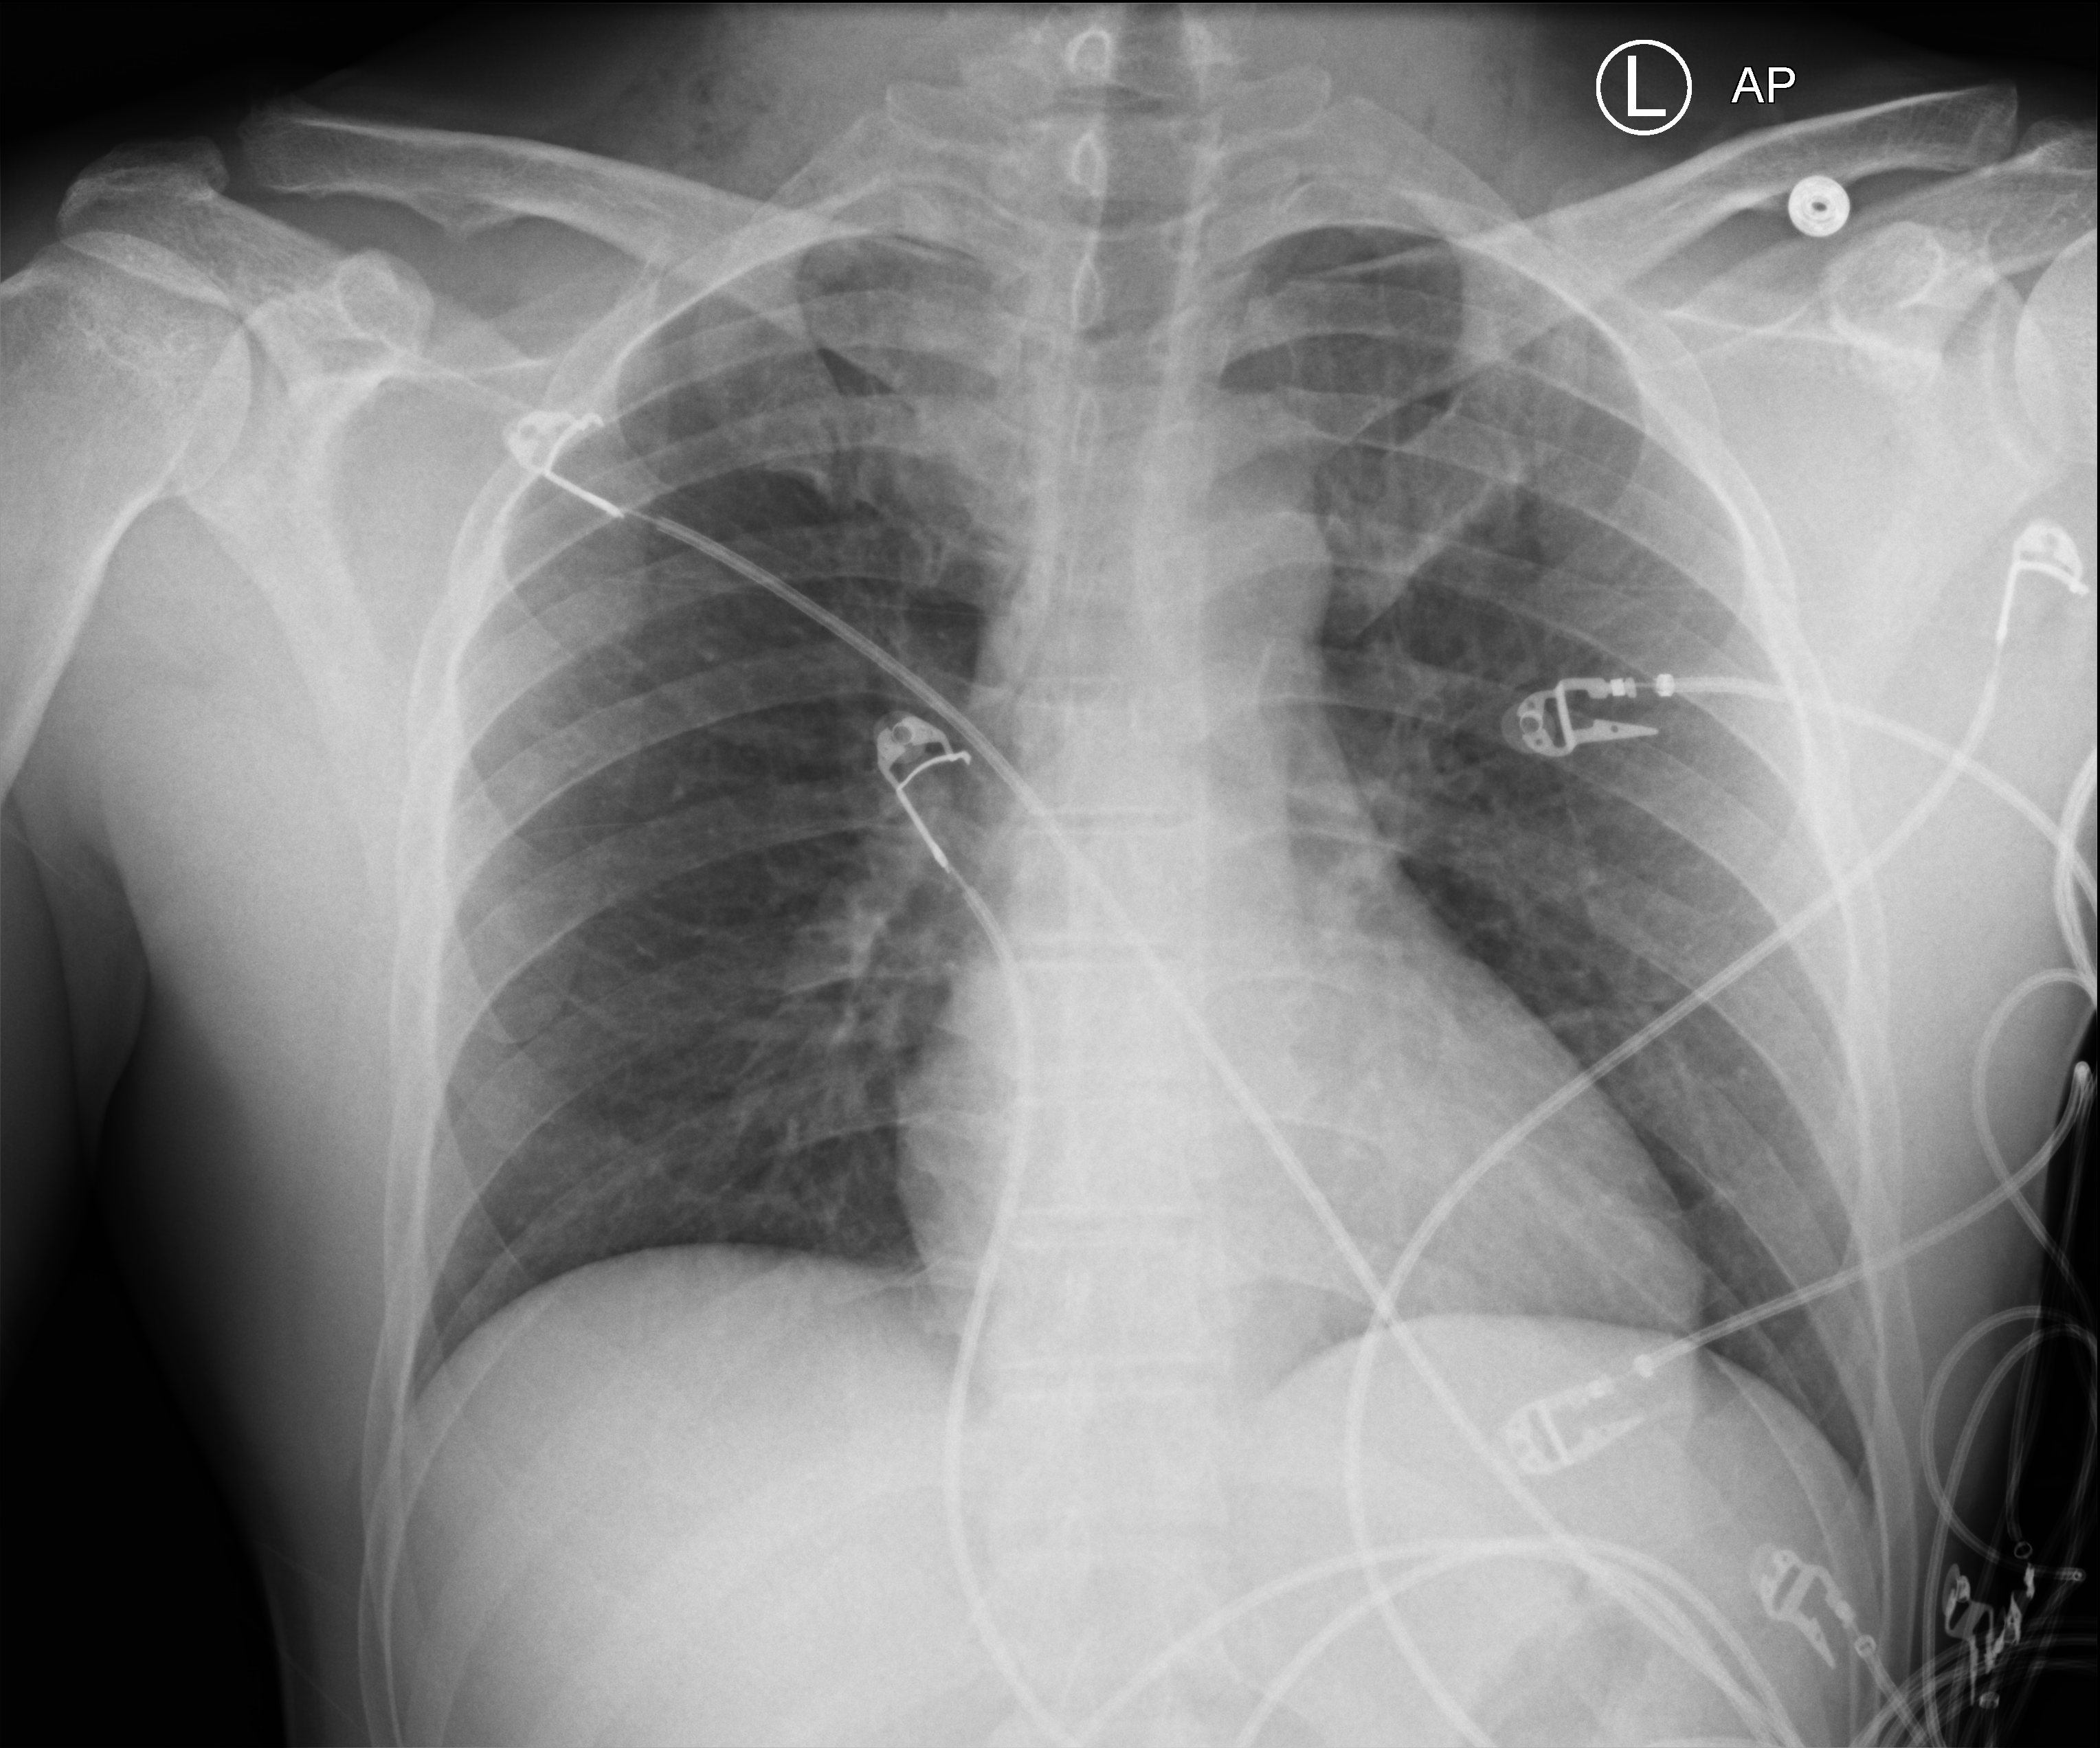
Chest X-ray (portable). Patient hospitalised with COVID-19; male, aged 18–59 years.
Hospital-stay facts (about this admission, not read from this image; timing relative to this image not recorded): other chronic lung disease (admission record): no; length of hospital stay: 3 days.